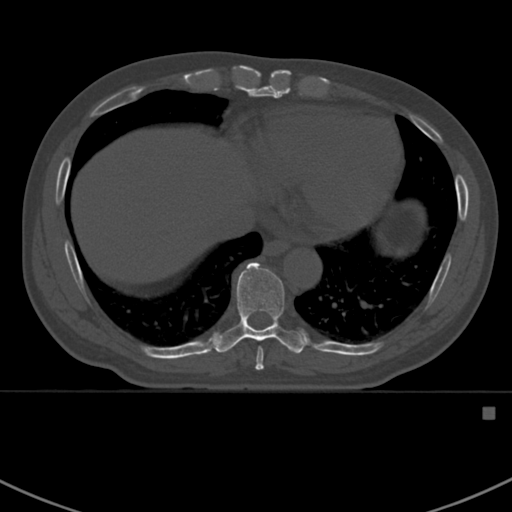
CT including the spine, one axial slice. Position 385 of 412 along the scan axis. Reconstruction kernel Br40s. Bone window (W 1800 / L 400 HU). 512 × 512 image matrix, field of view 358 × 358 mm. Patient: male, 59 years. From the clinical record (not read from this slice): primary cancer: prostate.
Structures marked on this image (semi-automatic segmentation, software-assisted and operator-edited):
- T8 vertebra: bounding box <255,347,264,371> (left, top, right, bottom; pixels)
- T9 vertebra: <213,262,309,354>